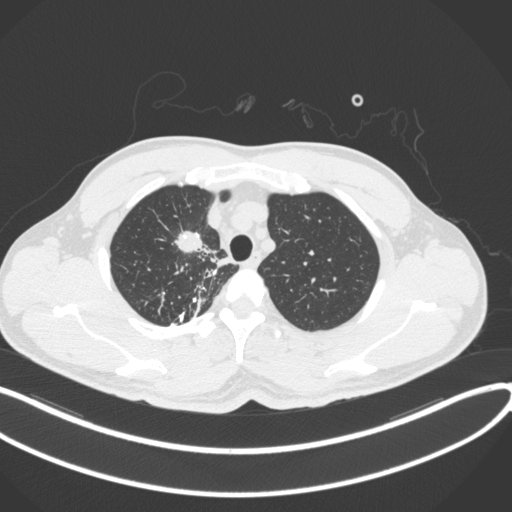
Chest CT, one axial slice. Position 309 of 391 along the scan axis. Reconstruction kernel B31f. Lung window (W 1500 / L -600 HU). 512 × 512 image matrix, field of view 400 × 400 mm. Male patient, age 48 years. Case-level facts recorded for this patient, not image findings: clinical TNM (as recorded): T1c N1 M1.
Structures marked on this image (rectangle marked by the reading radiologist):
- lung tumour (recorded histology: adenocarcinoma): bounding box <169,228,208,261> (left, top, right, bottom; pixels)